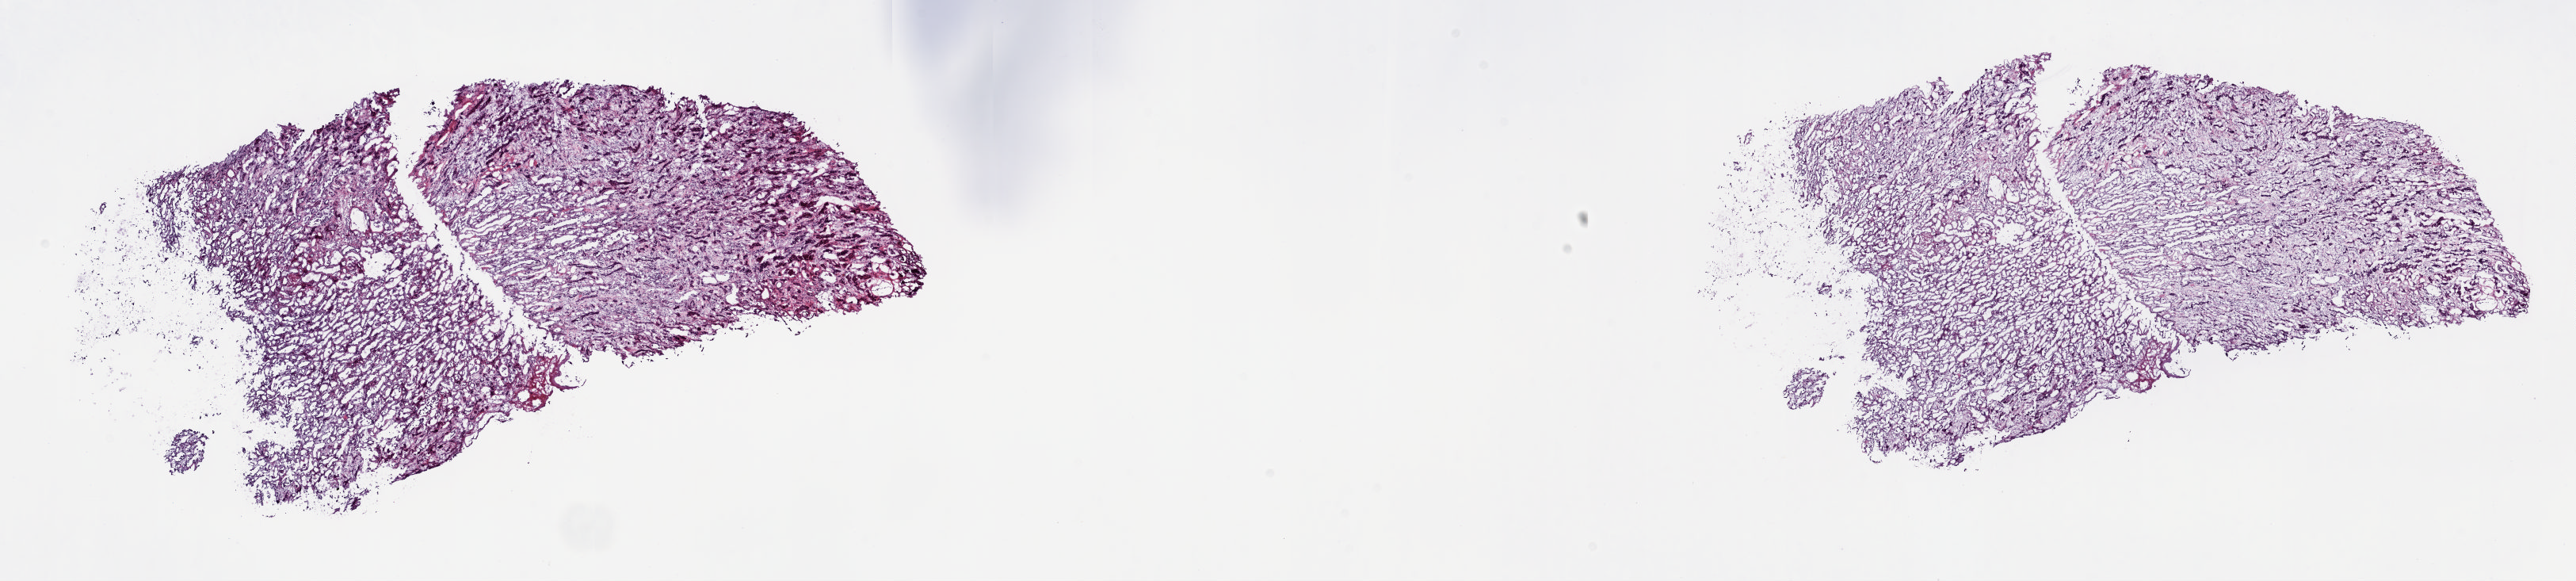
Digitized H&E tissue section (whole slide), a low-resolution overview of the entire scanned area, about 25.8 x 5.8 mm (slide scanned at 20x); frozen section from the top of the tissue portion; solid tissue normal (non-tumour tissue) sample from the kidney. Male patient; age at initial diagnosis 85 years.
This section: solid tissue normal (non-tumour) sample from the same patient. Patient diagnosis: Papillary adenocarcinoma, NOS.